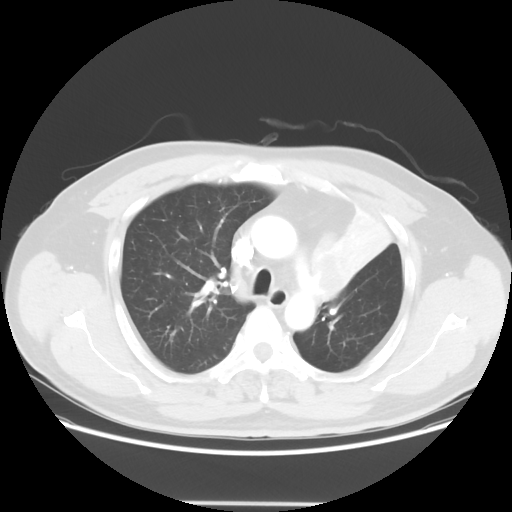
Chest CT, one axial slice. Position 43 of 62 along the scan axis. 120 kVp. Lung window (W 1500 / L -600 HU). 512 × 512 image matrix, field of view 403 × 403 mm. Male patient, age 49 years. From the clinical record (not read from this slice): clinical TNM (as recorded): T3 N3 M1c.
Structures marked on this image (rectangle marked by the reading radiologist):
- lung tumour (recorded histology: squamous cell carcinoma): bounding box [x1, y1, x2, y2] px = [308, 237, 357, 306]